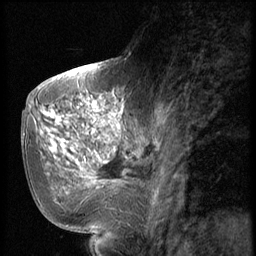
Breast MRI (dynamic contrast-enhanced), one sagittal slice; slice 25 of 56 in the series (ordered by position); dynamic contrast-enhanced series, image 2 of 2 at this slice position (ordered by acquisition); 1.5 T; TE 4.2 ms, TR 9 ms; 2.5 mm slice thickness; 256 × 256 image matrix. Patient: female, 51 years. Case-level facts recorded for this patient, not image findings: setting: breast cancer imaged before/during neoadjuvant chemotherapy; receptor status: triple-negative.
Outlined on this slice (semi-automatically segmented with operator editing):
- analysis volume of interest (the breast-tissue region the enhancement analysis was run in; not a lesion): bounding box [x1, y1, x2, y2] px = [60, 98, 147, 197]
- tumour enhancement mask (voxels above the 140 % enhancement threshold inside the analysis volume of interest): [62, 100, 123, 187]